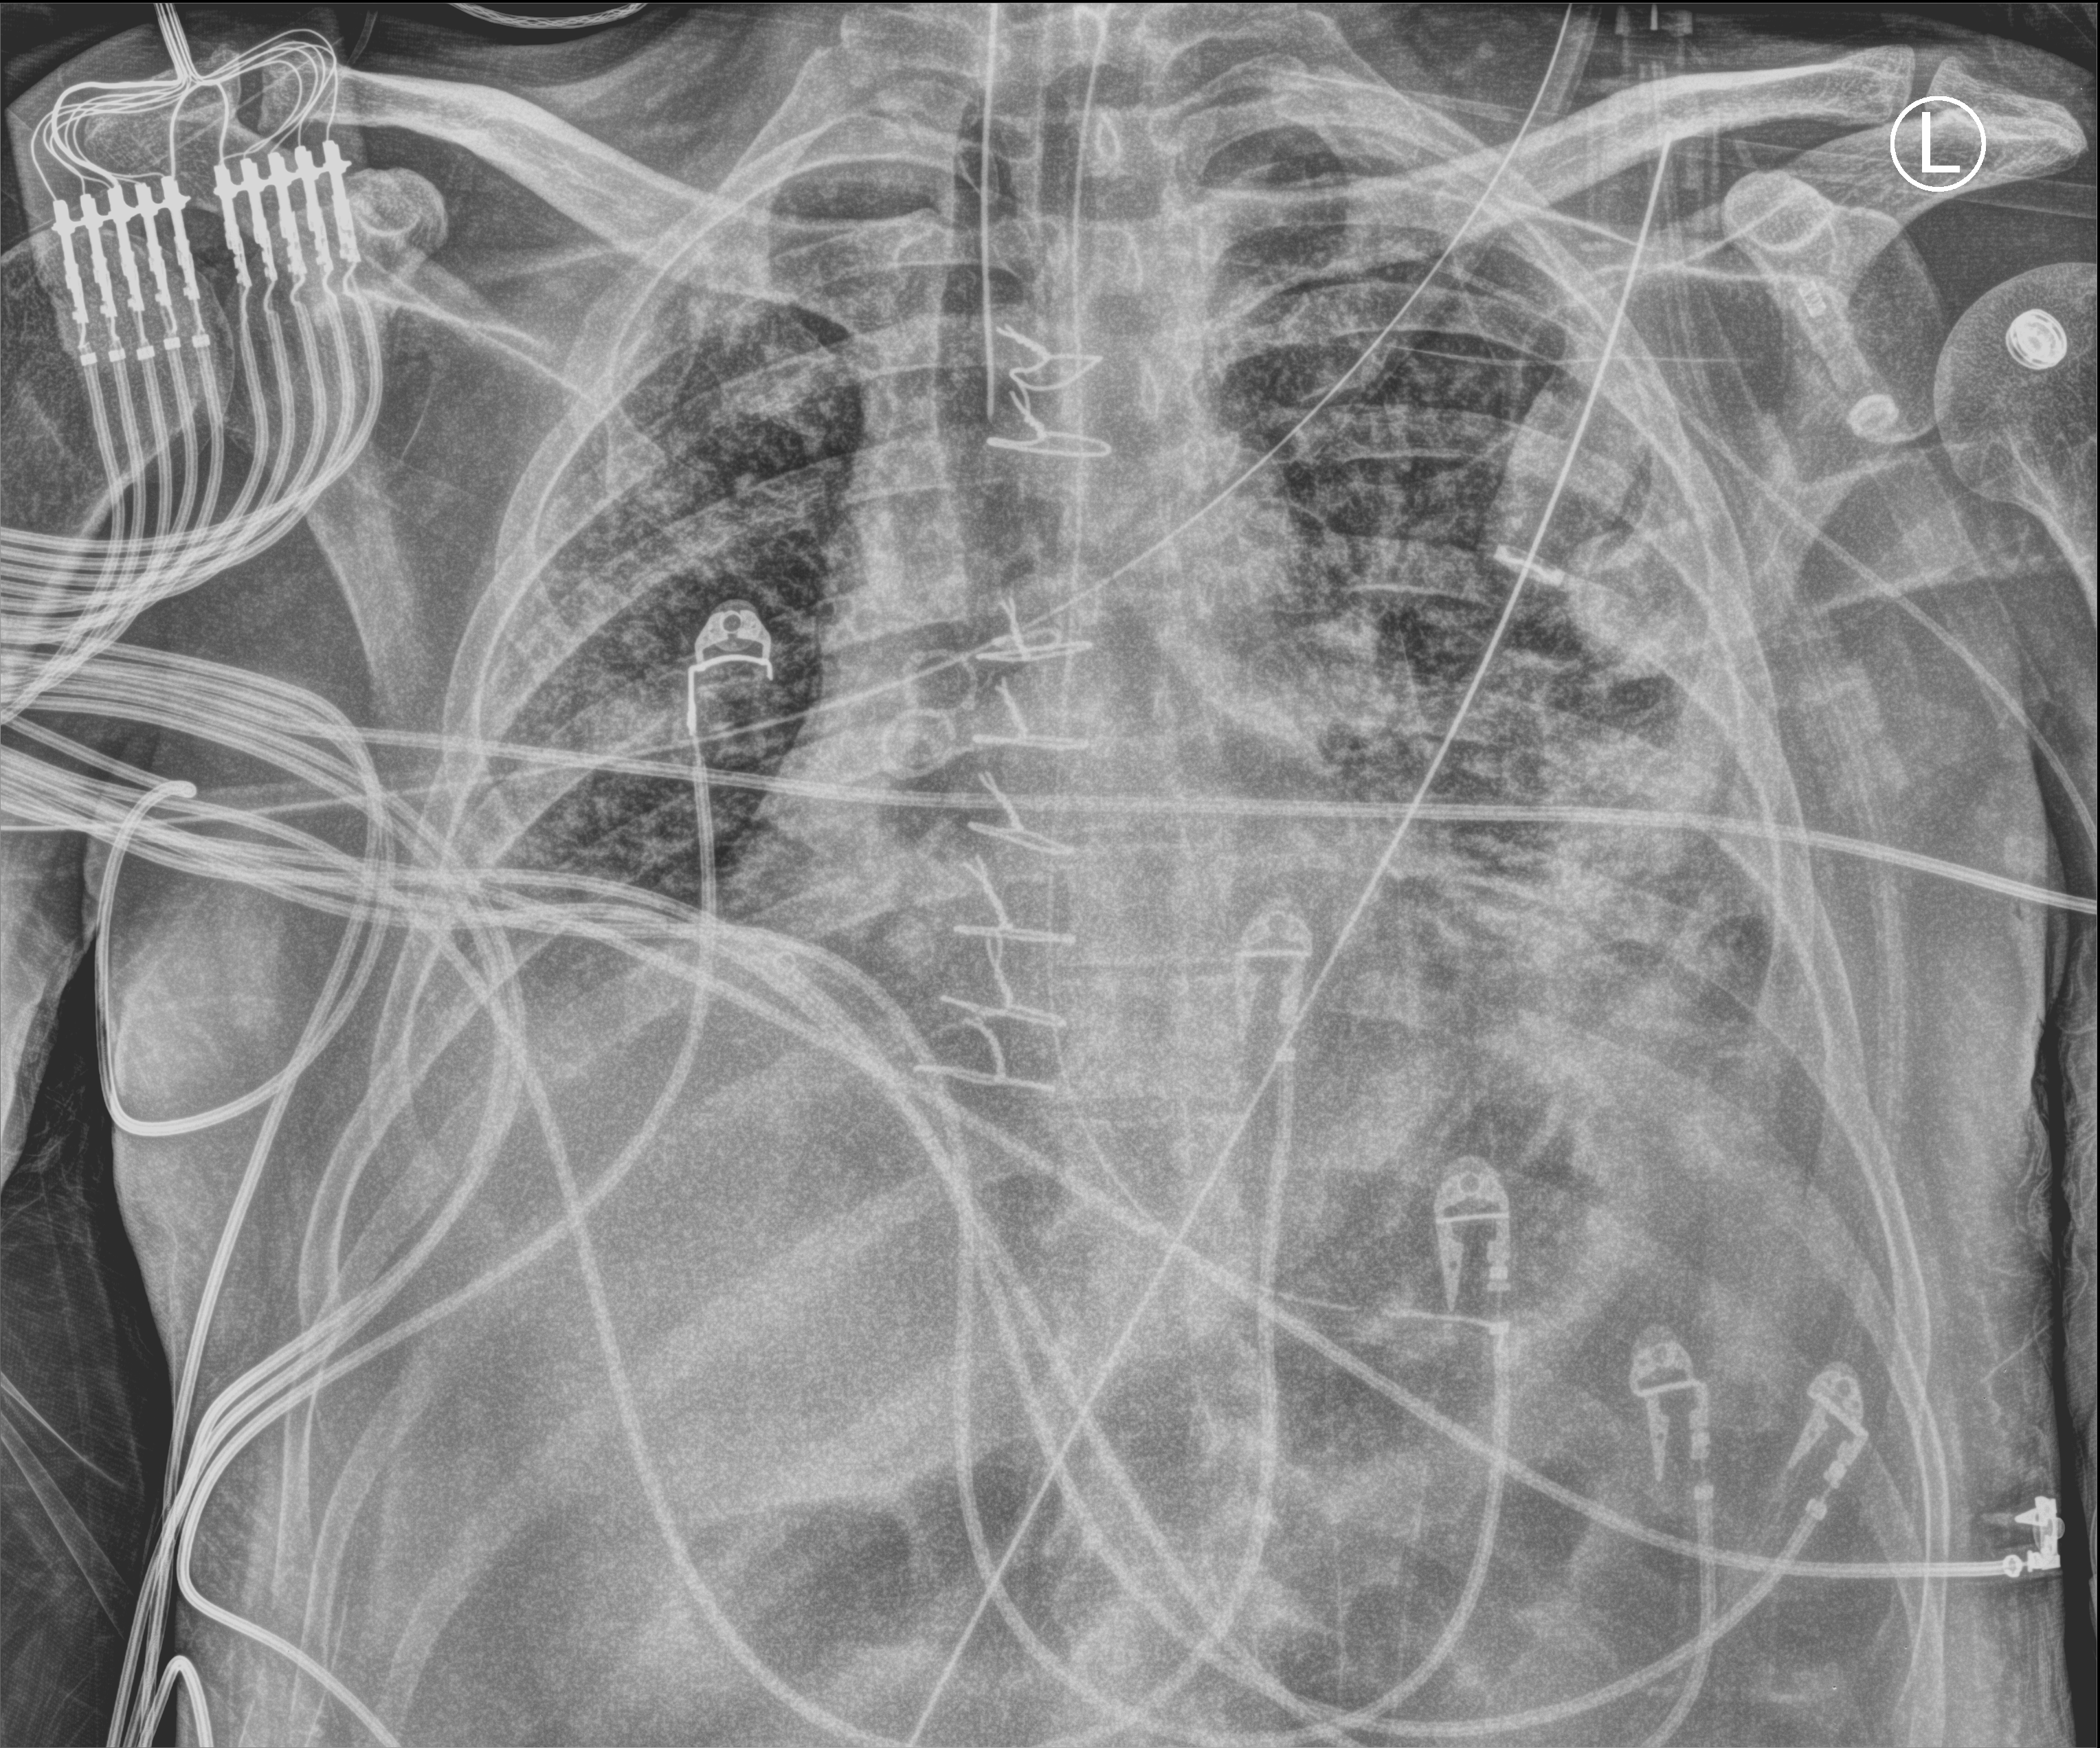
Bedside chest radiograph (computed radiography). Male patient hospitalised with COVID-19, age 18–59 years.
From the hospital-stay record, not from the radiograph (when in the stay this image was taken is not recorded): smoking status (admission record): former.